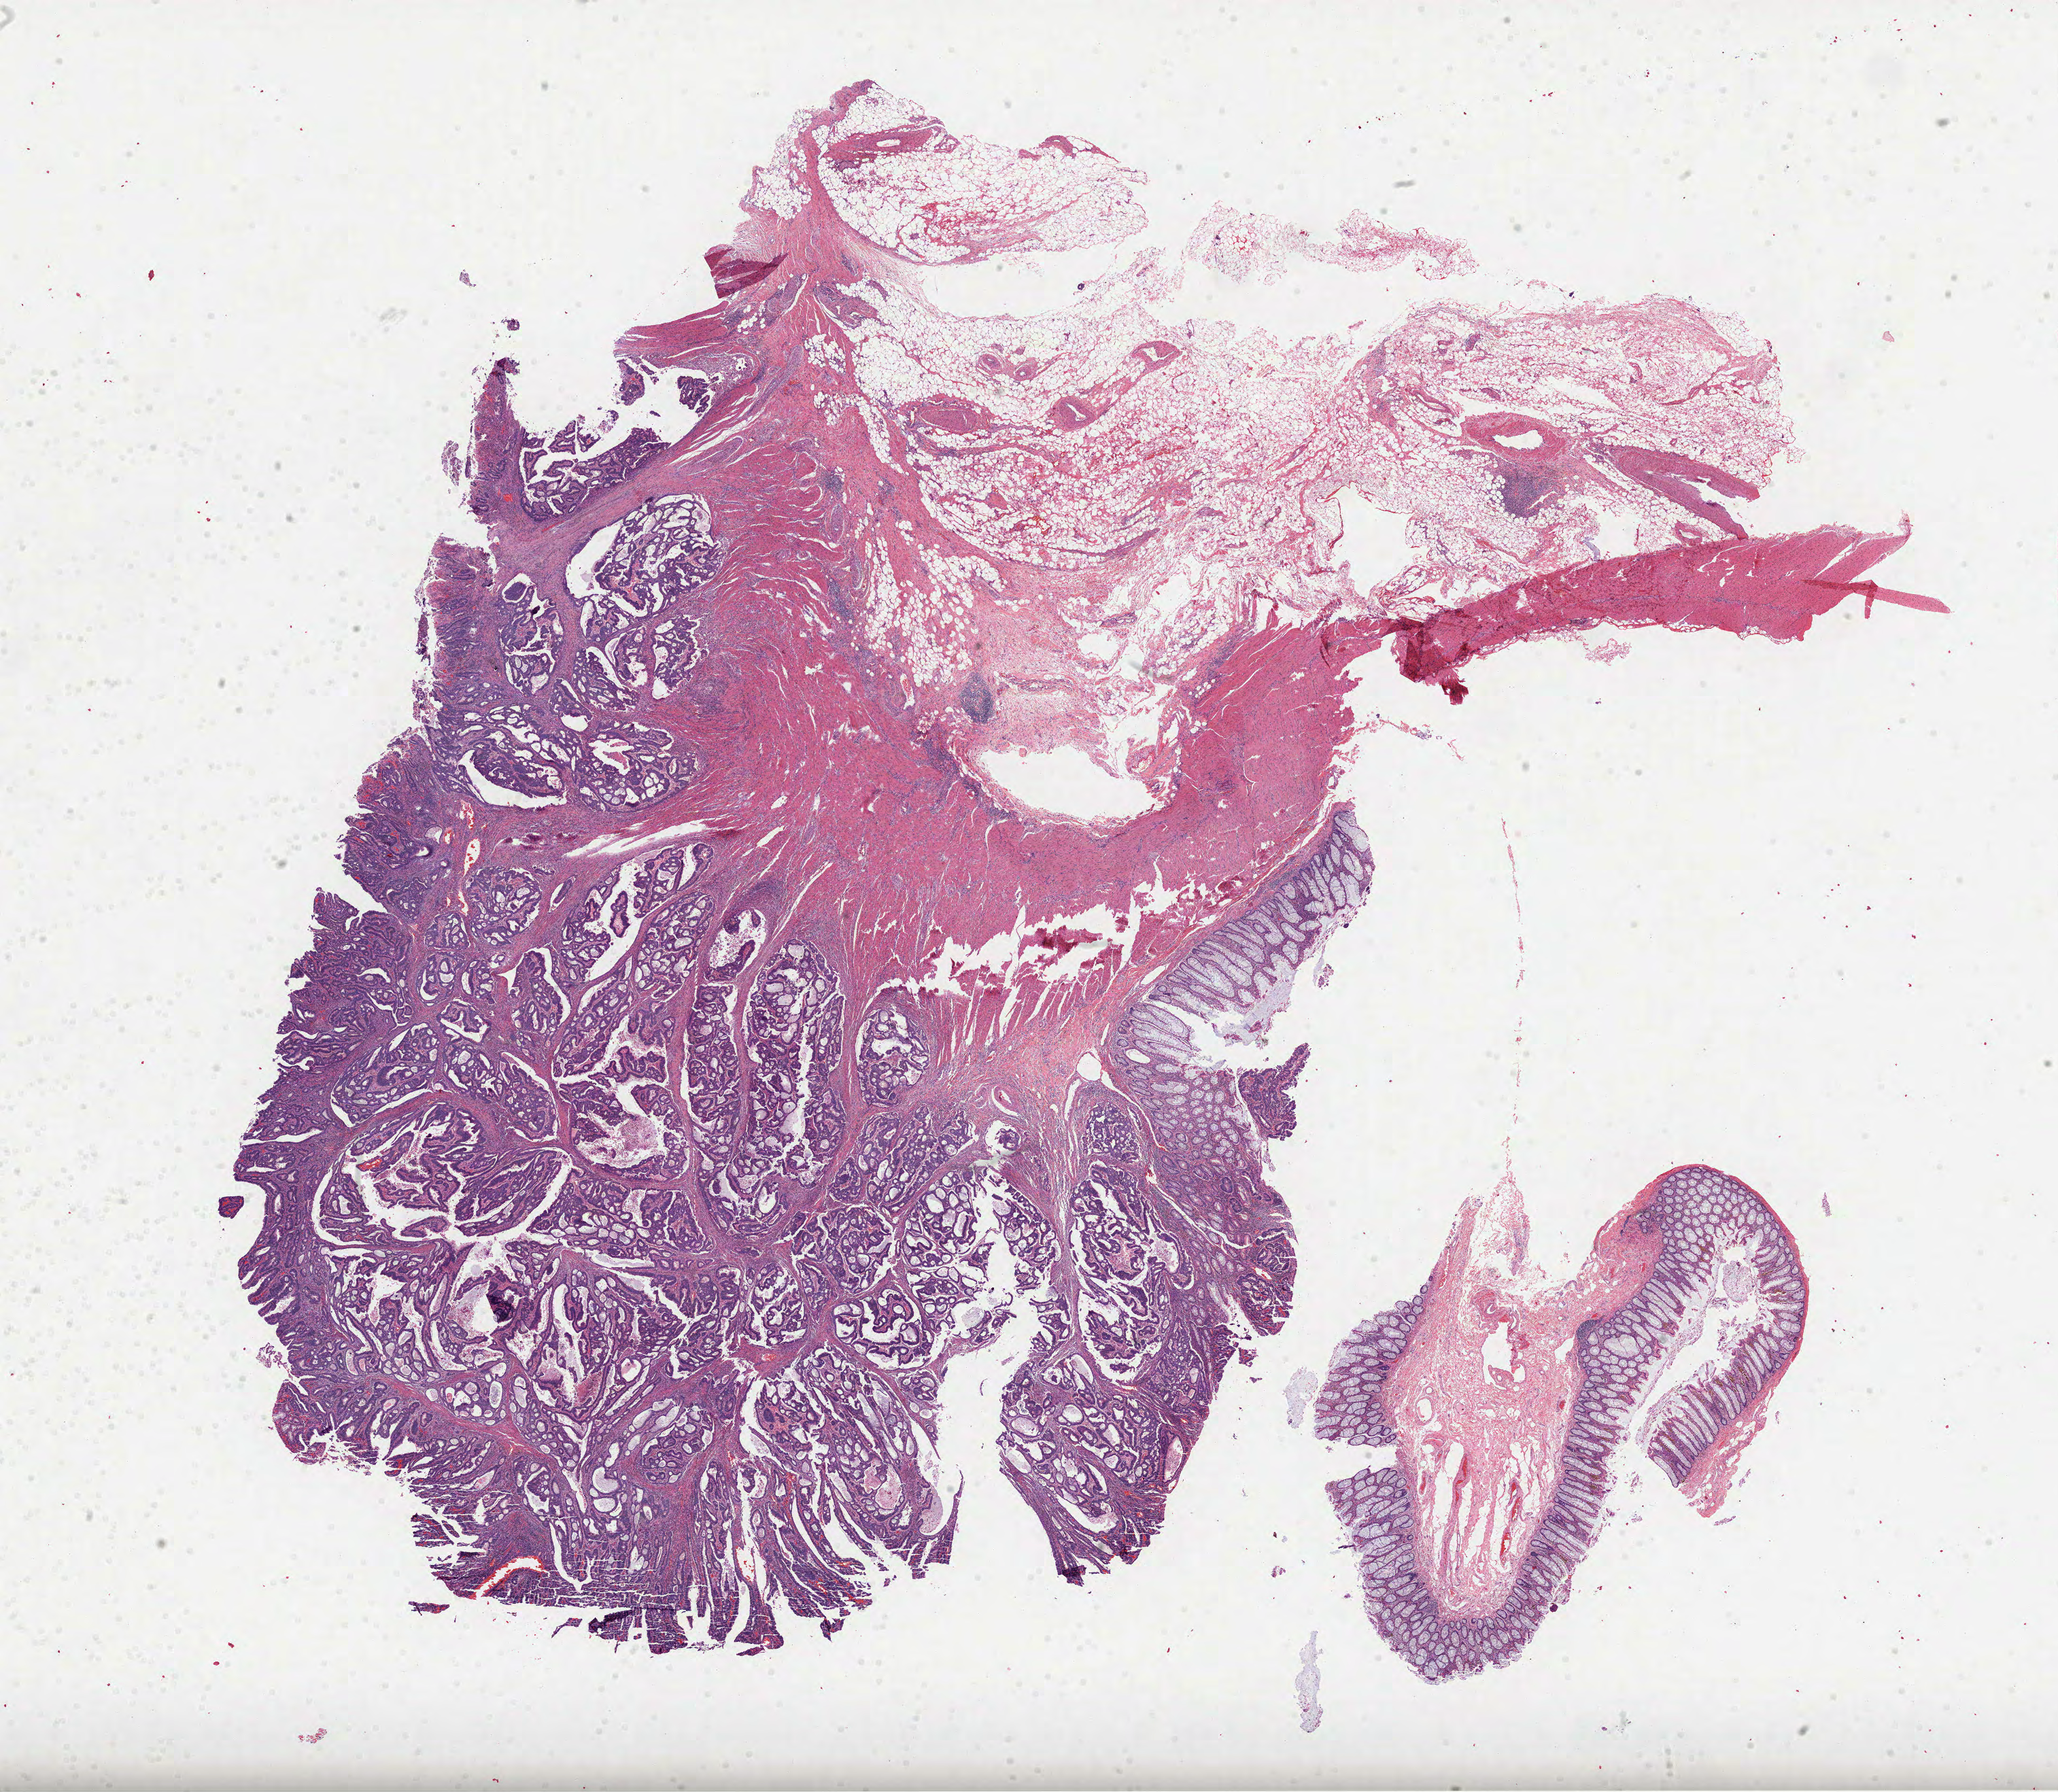
Digitized H&E-stained tissue section (whole slide), low-resolution overview of the scanned area, about 24.4 x 21.3 mm, formalin-fixed paraffin-embedded (FFPE) diagnostic section, sample: primary tumour, colon. Female, age 46 years at initial diagnosis.
AJCC pathologic stage: IIA. Diagnosis: Adenocarcinoma, NOS (sigmoid colon).